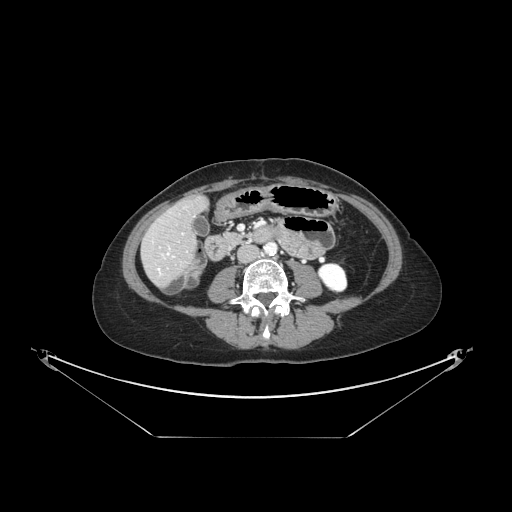
Contrast-enhanced abdominal CT, one axial slice. Slice 38 of 148 in the series (ordered by position). Reconstruction kernel STANDARD. 120 kVp. Intravenous contrast given. Soft-tissue window (W 400 / L 40 HU). 2.5 mm slice thickness. 512 × 512 image matrix. Female patient, age 73 years. Case-level facts recorded for this patient, not image findings: diagnosis: colorectal cancer liver metastases, imaged before liver resection.
Structures marked on this image (expert manual segmentation):
- hepatic veins: box from (x=158, y=253) to (x=169, y=271) px
- liver: (x=143, y=198)–(x=206, y=285)
- planned liver remnant (the part of the liver to remain after resection): (x=161, y=198)–(x=206, y=240)